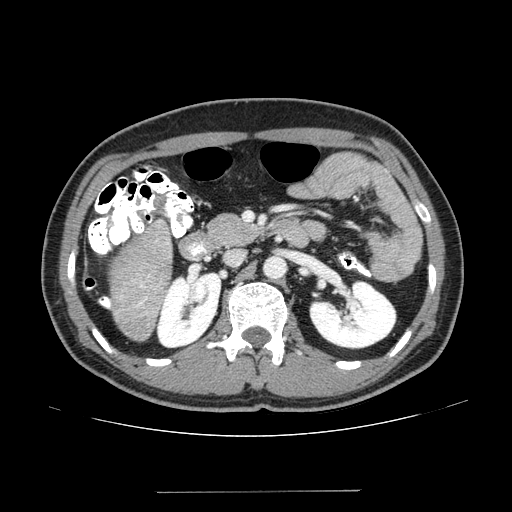
Contrast-enhanced abdominal CT (liver protocol), one axial slice. Slice 61 of 131 in the series (ordered by position). Reconstruction kernel STANDARD. 100 kVp. One of 2 acquisitions stored at this slice position. Soft-tissue window (W 400 / L 40 HU). 512 × 512 image matrix, field of view 380 × 380 mm. From the clinical record (not read from this slice): diagnosis: hepatocellular carcinoma (patient treated with transarterial chemoembolisation; whether this scan precedes or follows treatment is not stated here); TNM stage (as recorded): Stage-I; Child-Pugh class: A; tumour differentiation: poorly differentiated.
Annotated regions visible in this slice (semi-automatically segmented with operator editing):
- liver parenchyma outside the tumour (the mass and vessels are separate outlines, so this box may not span the whole liver): bounding box <142,308,156,330> (left, top, right, bottom; pixels)